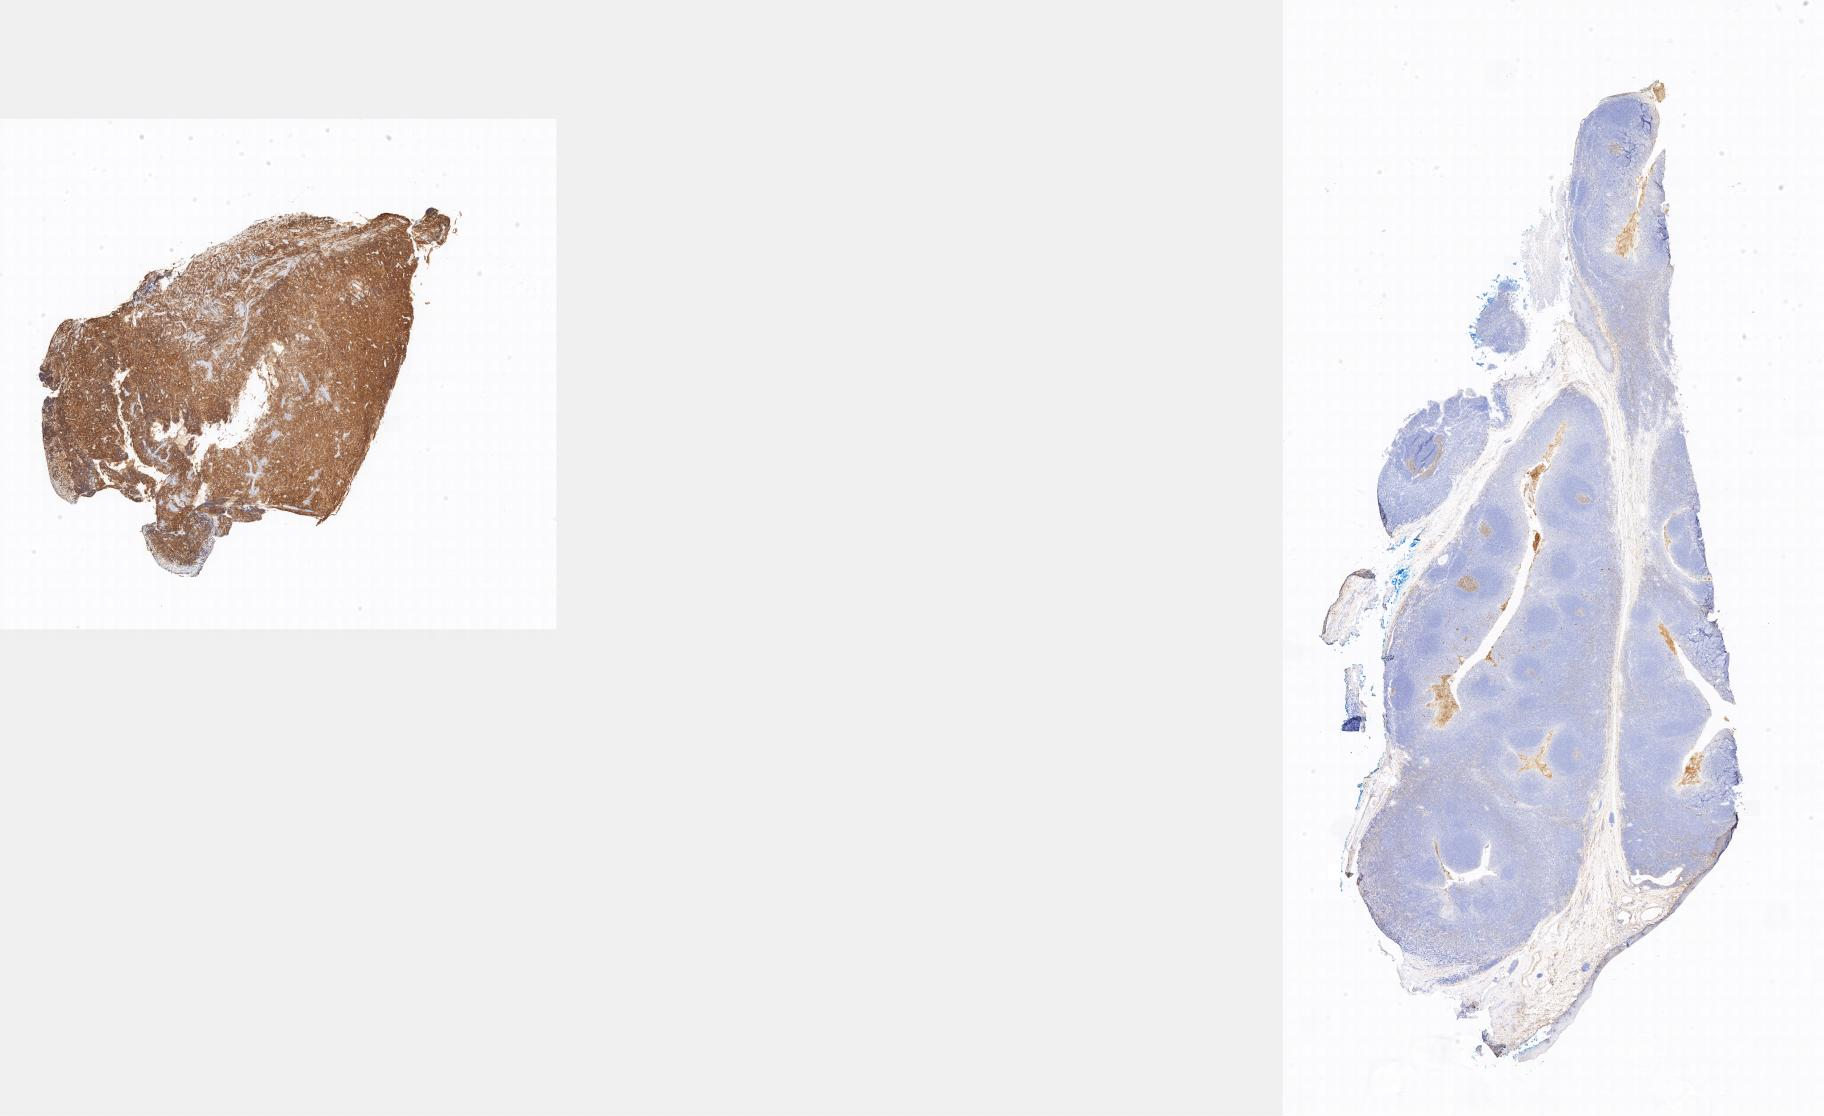
IHC for CD10, whole-slide image, whole scanned area shown as a low-resolution overview; specimen: tumor tissue; anatomic site: ovary. Female, age 3 years at initial diagnosis.
Diagnosis: Burkitt lymphoma, NOS.